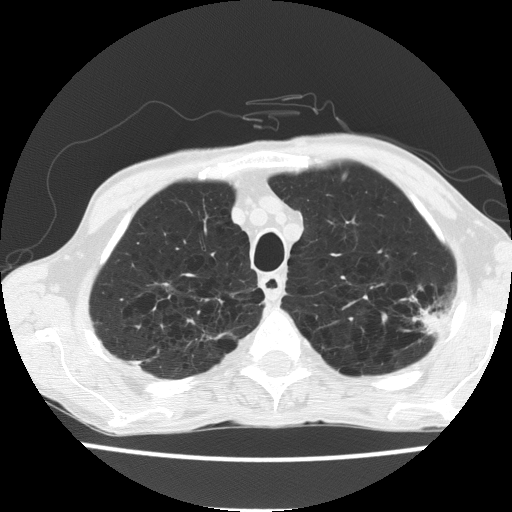
Low-dose screening chest CT, axial slice. Baseline screening round. Lung window (W 1500 / L -600 HU). Lung (sharp) reconstruction kernel (FC51). Male, age 60 years at enrolment. Current smoker at enrolment.
Expert reader's lesion annotation, box from (x=395, y=284) to (x=458, y=348) px. No non-calcified nodule or mass ≥4 mm was recorded by the screening reader at this exam. Official screen result: negative screen, minor abnormalities not suspicious for lung cancer. Lung cancer was diagnosed 490 days after this screen (after the second annual screen): bronchiolo-alveolar carcinoma, mucinous, left upper lobe, stage IV (AJCC 6th edition).